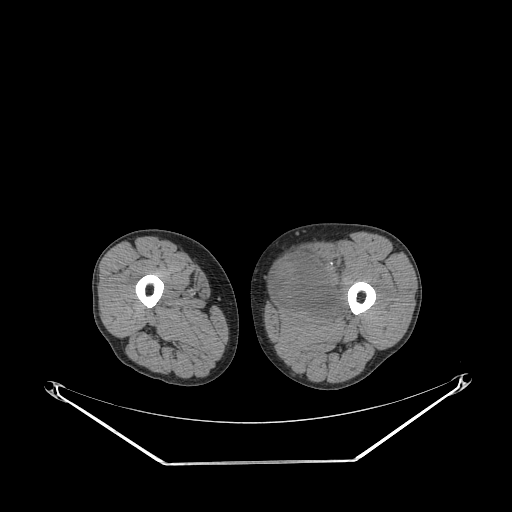
CT of an extremity soft-tissue mass (from a PET/CT study), one axial slice. Position 233 of 267 along the scan axis. Reconstruction kernel STANDARD. Soft-tissue window (W 400 / L 40 HU). 512 × 512 image matrix, field of view 500 × 500 mm. Male patient. From the clinical record (not read from this slice): histological type: pleiomorphic liposarcoma; grade: high; site of the primary tumour: left thigh.
Annotated regions visible in this slice (expert contour drawn on MRI and transferred to this co-registered scan by the dataset authors):
- gross tumour volume including surrounding oedema: bounding box (x1, y1, x2, y2) in pixels: (274, 249, 346, 321)
- gross tumour volume (mass): (274, 253, 339, 314)